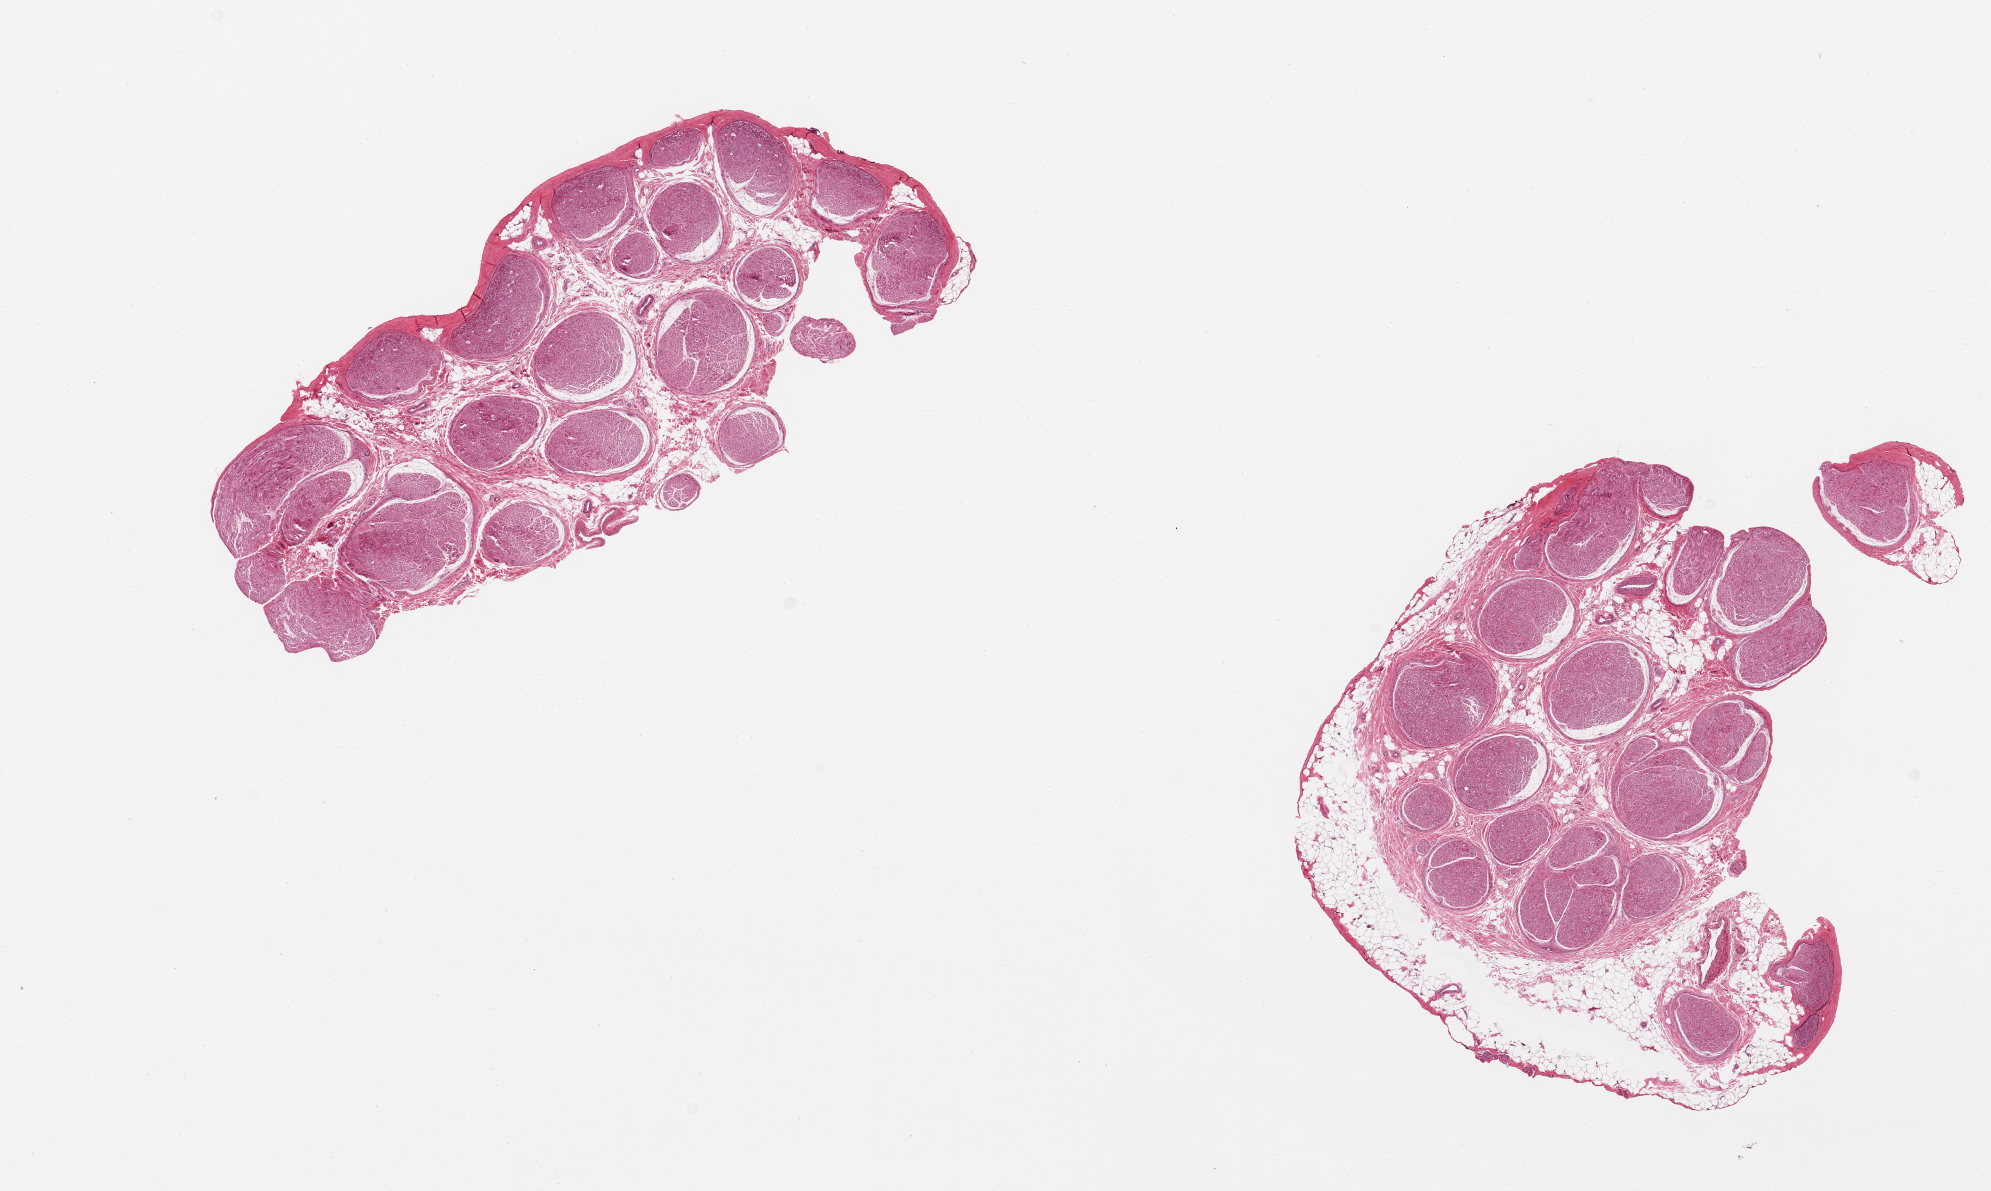
Digitized haematoxylin and eosin-stained section — shown as a low-resolution overview of the whole scanned area (about 15.8 x 9.4 mm); PAXgene-fixed, paraffin-embedded tissue; section of tibial nerve (target tissue); donor tissue sample. Donor: male.
- reviewer comment on this tissue sample: 2 pieces; 20% internal and external fat